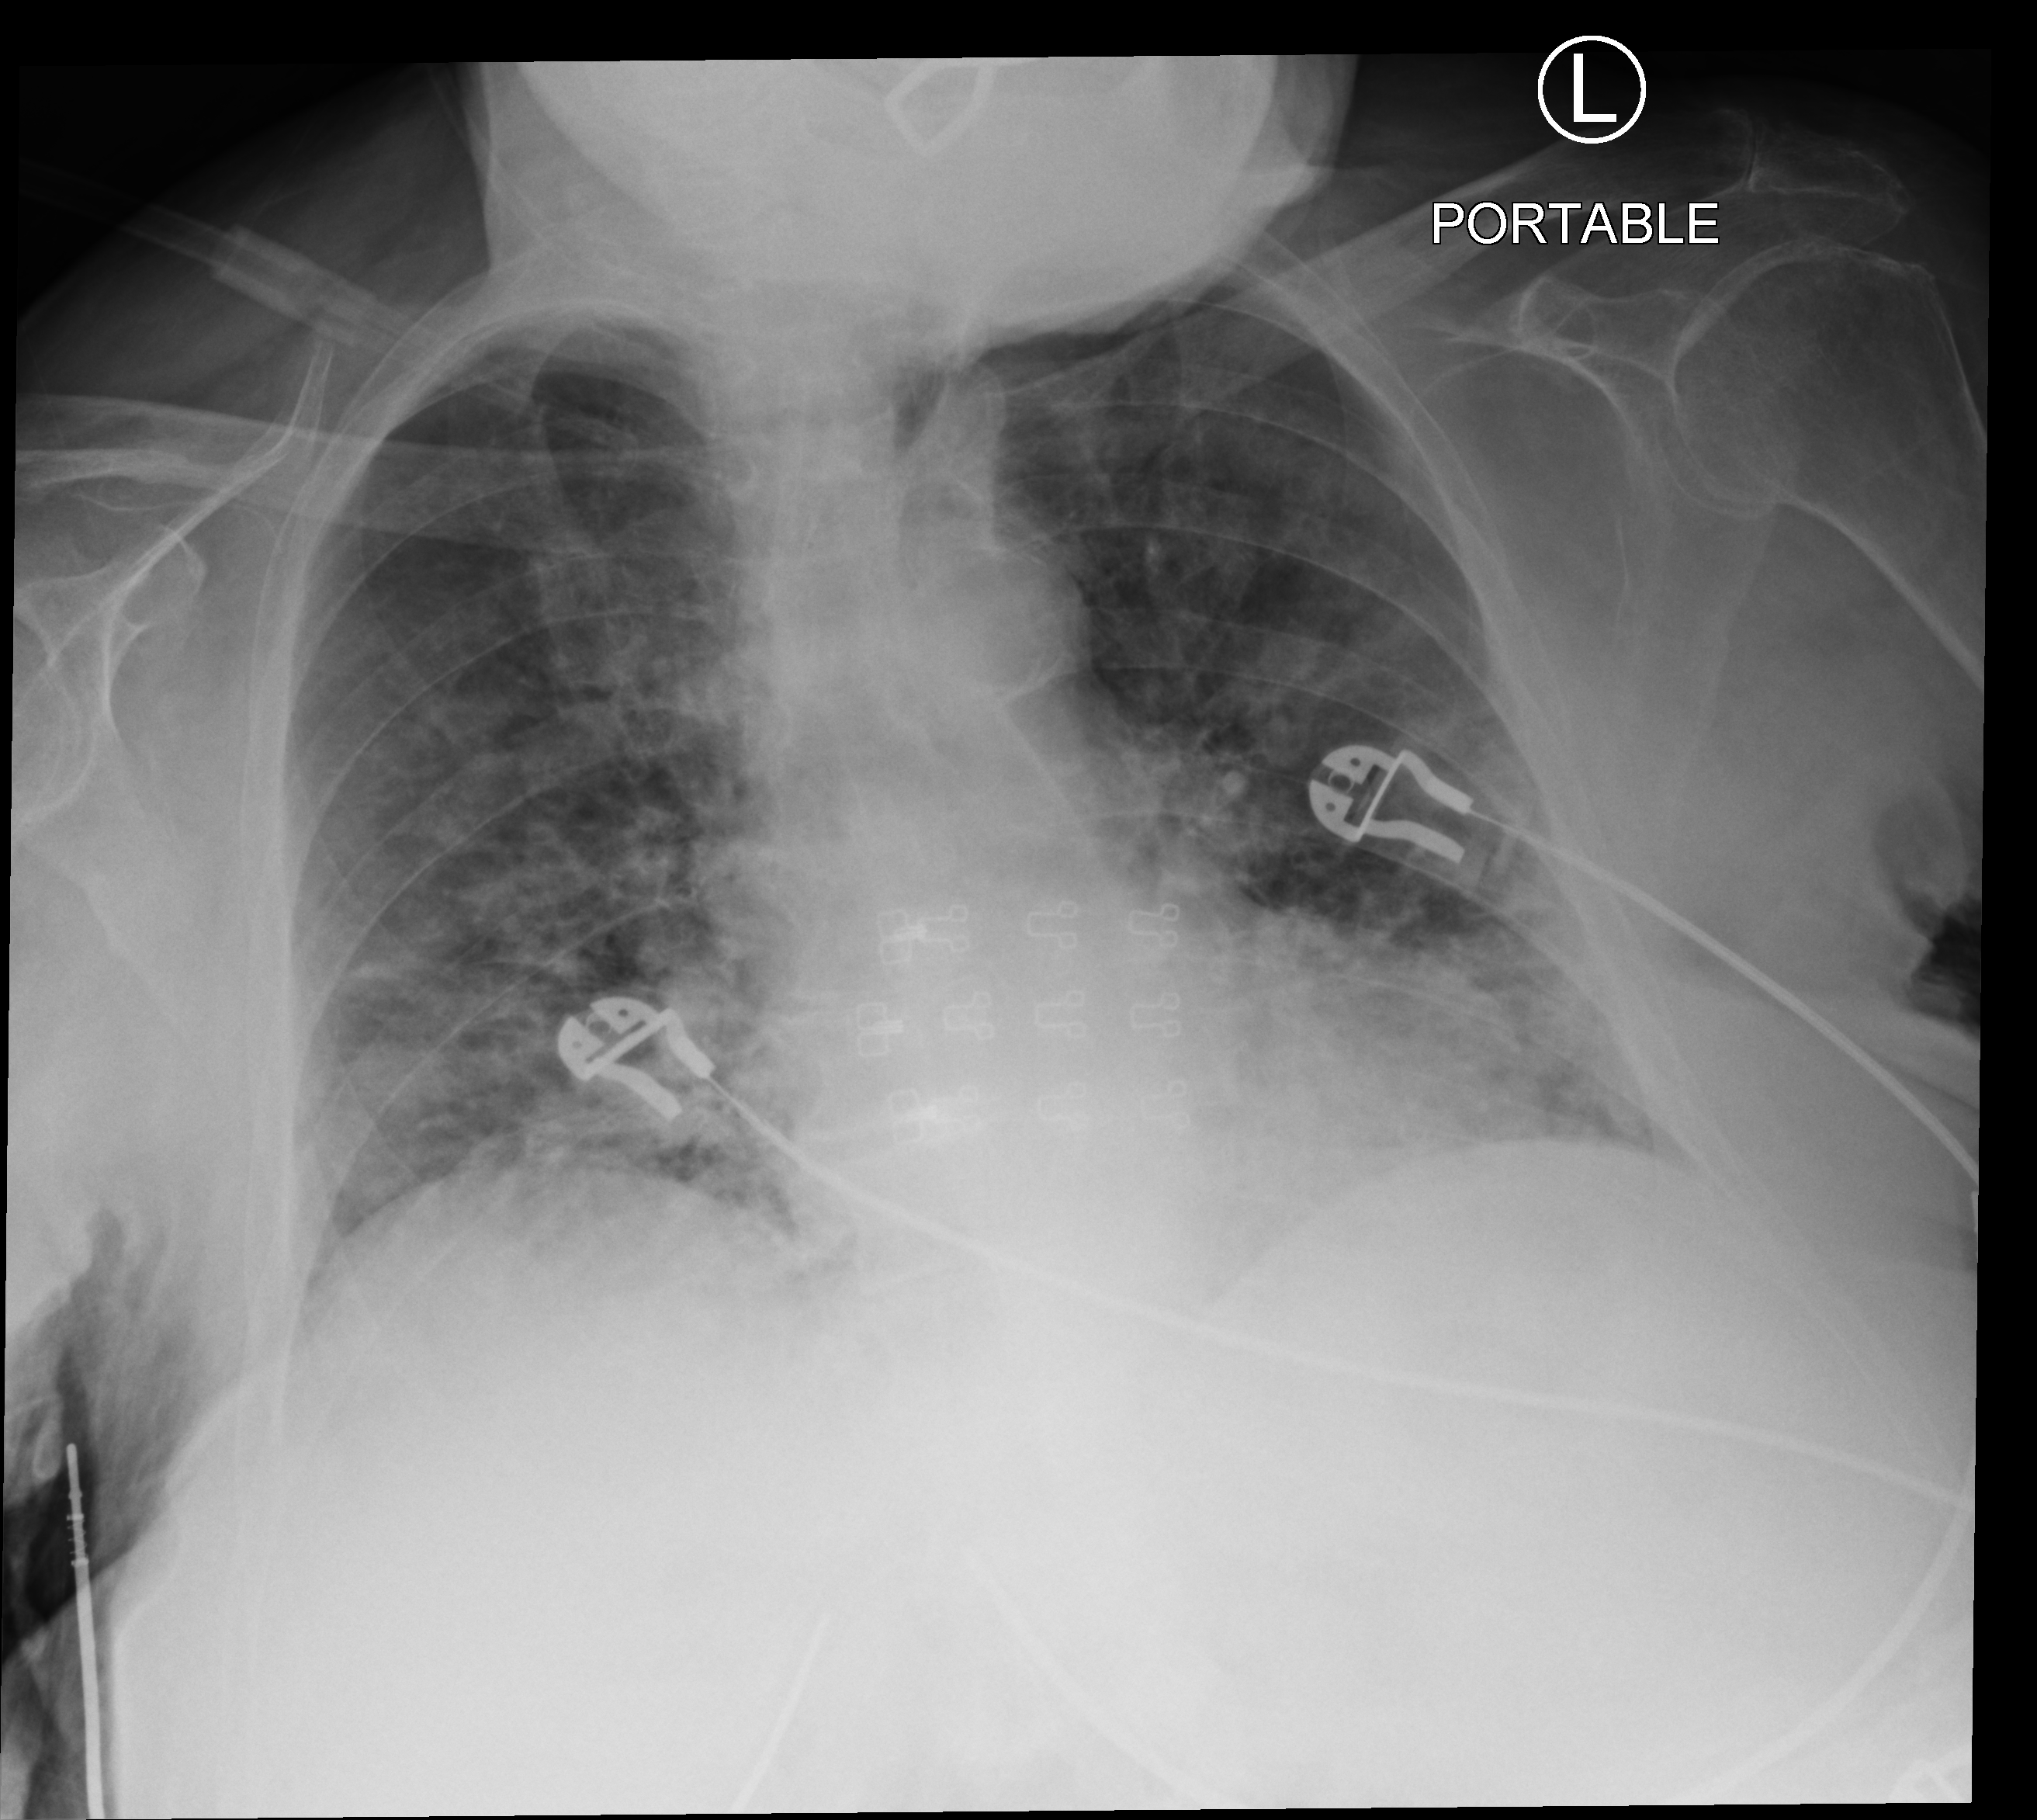
Chest X-ray (portable), anteroposterior (AP) projection. Female patient hospitalised with COVID-19, age 75–90 years.
From the hospital-stay record, not from the radiograph (when in the stay this image was taken is not recorded): length of hospital stay: 5 days.